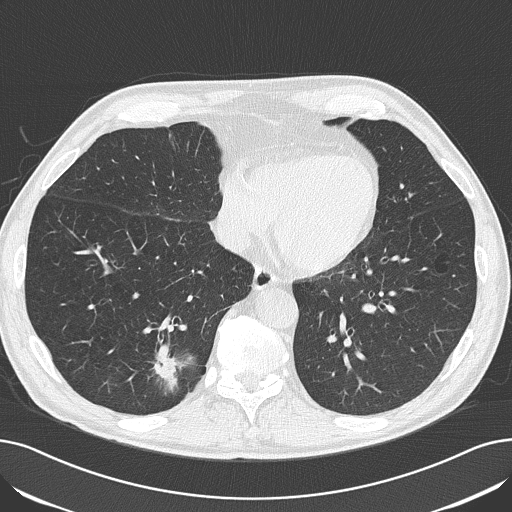
Low-dose screening chest CT, axial slice, first (baseline) screen, lung window (W 1500 / L -600 HU), 120 kVp, slice 124 of 182 in the series. Male participant, aged 71 years at enrolment. Current smoker at enrolment.
Expert-annotated lung lesion, bounding box (x1, y1, x2, y2) in pixels: (134, 331, 195, 396). The exam's reader record, not a measurement of the box and not confirmed to be the same lesion: non-calcified nodule or mass ≥4 mm, right lower lobe, 14 × 14 mm, spiculated (stellate) margins, soft tissue attenuation. Official screen result: positive, change unspecified: nodule(s) >= 4 mm or enlarging nodule(s), mass(es), or other non-specific abnormalities suspicious for lung cancer. Later outcome: lung cancer diagnosed 145 days after this screen — adenocarcinoma, NOS, right lower lobe, moderately differentiated (G2), stage IA (AJCC 6th edition), 24 mm at pathology.